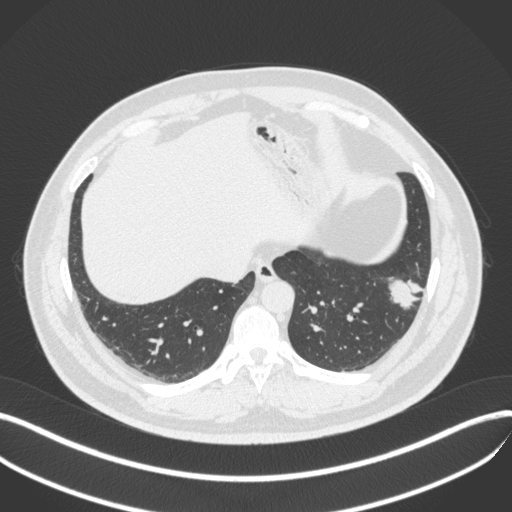
Chest CT, one axial slice. Position 115 of 420 along the scan axis. 120 kVp. Lung window (W 1500 / L -600 HU). 1 mm slice thickness. 512 × 512 image matrix. Male patient, age 39 years. Case-level facts recorded for this patient, not image findings: clinical TNM (as recorded): T2a N0 M0; histopathological grade: G2-3.
Outlined on this slice (rectangle marked by the reading radiologist):
- lung tumour (recorded histology: adenocarcinoma): bounding box <381,271,427,314> (left, top, right, bottom; pixels)